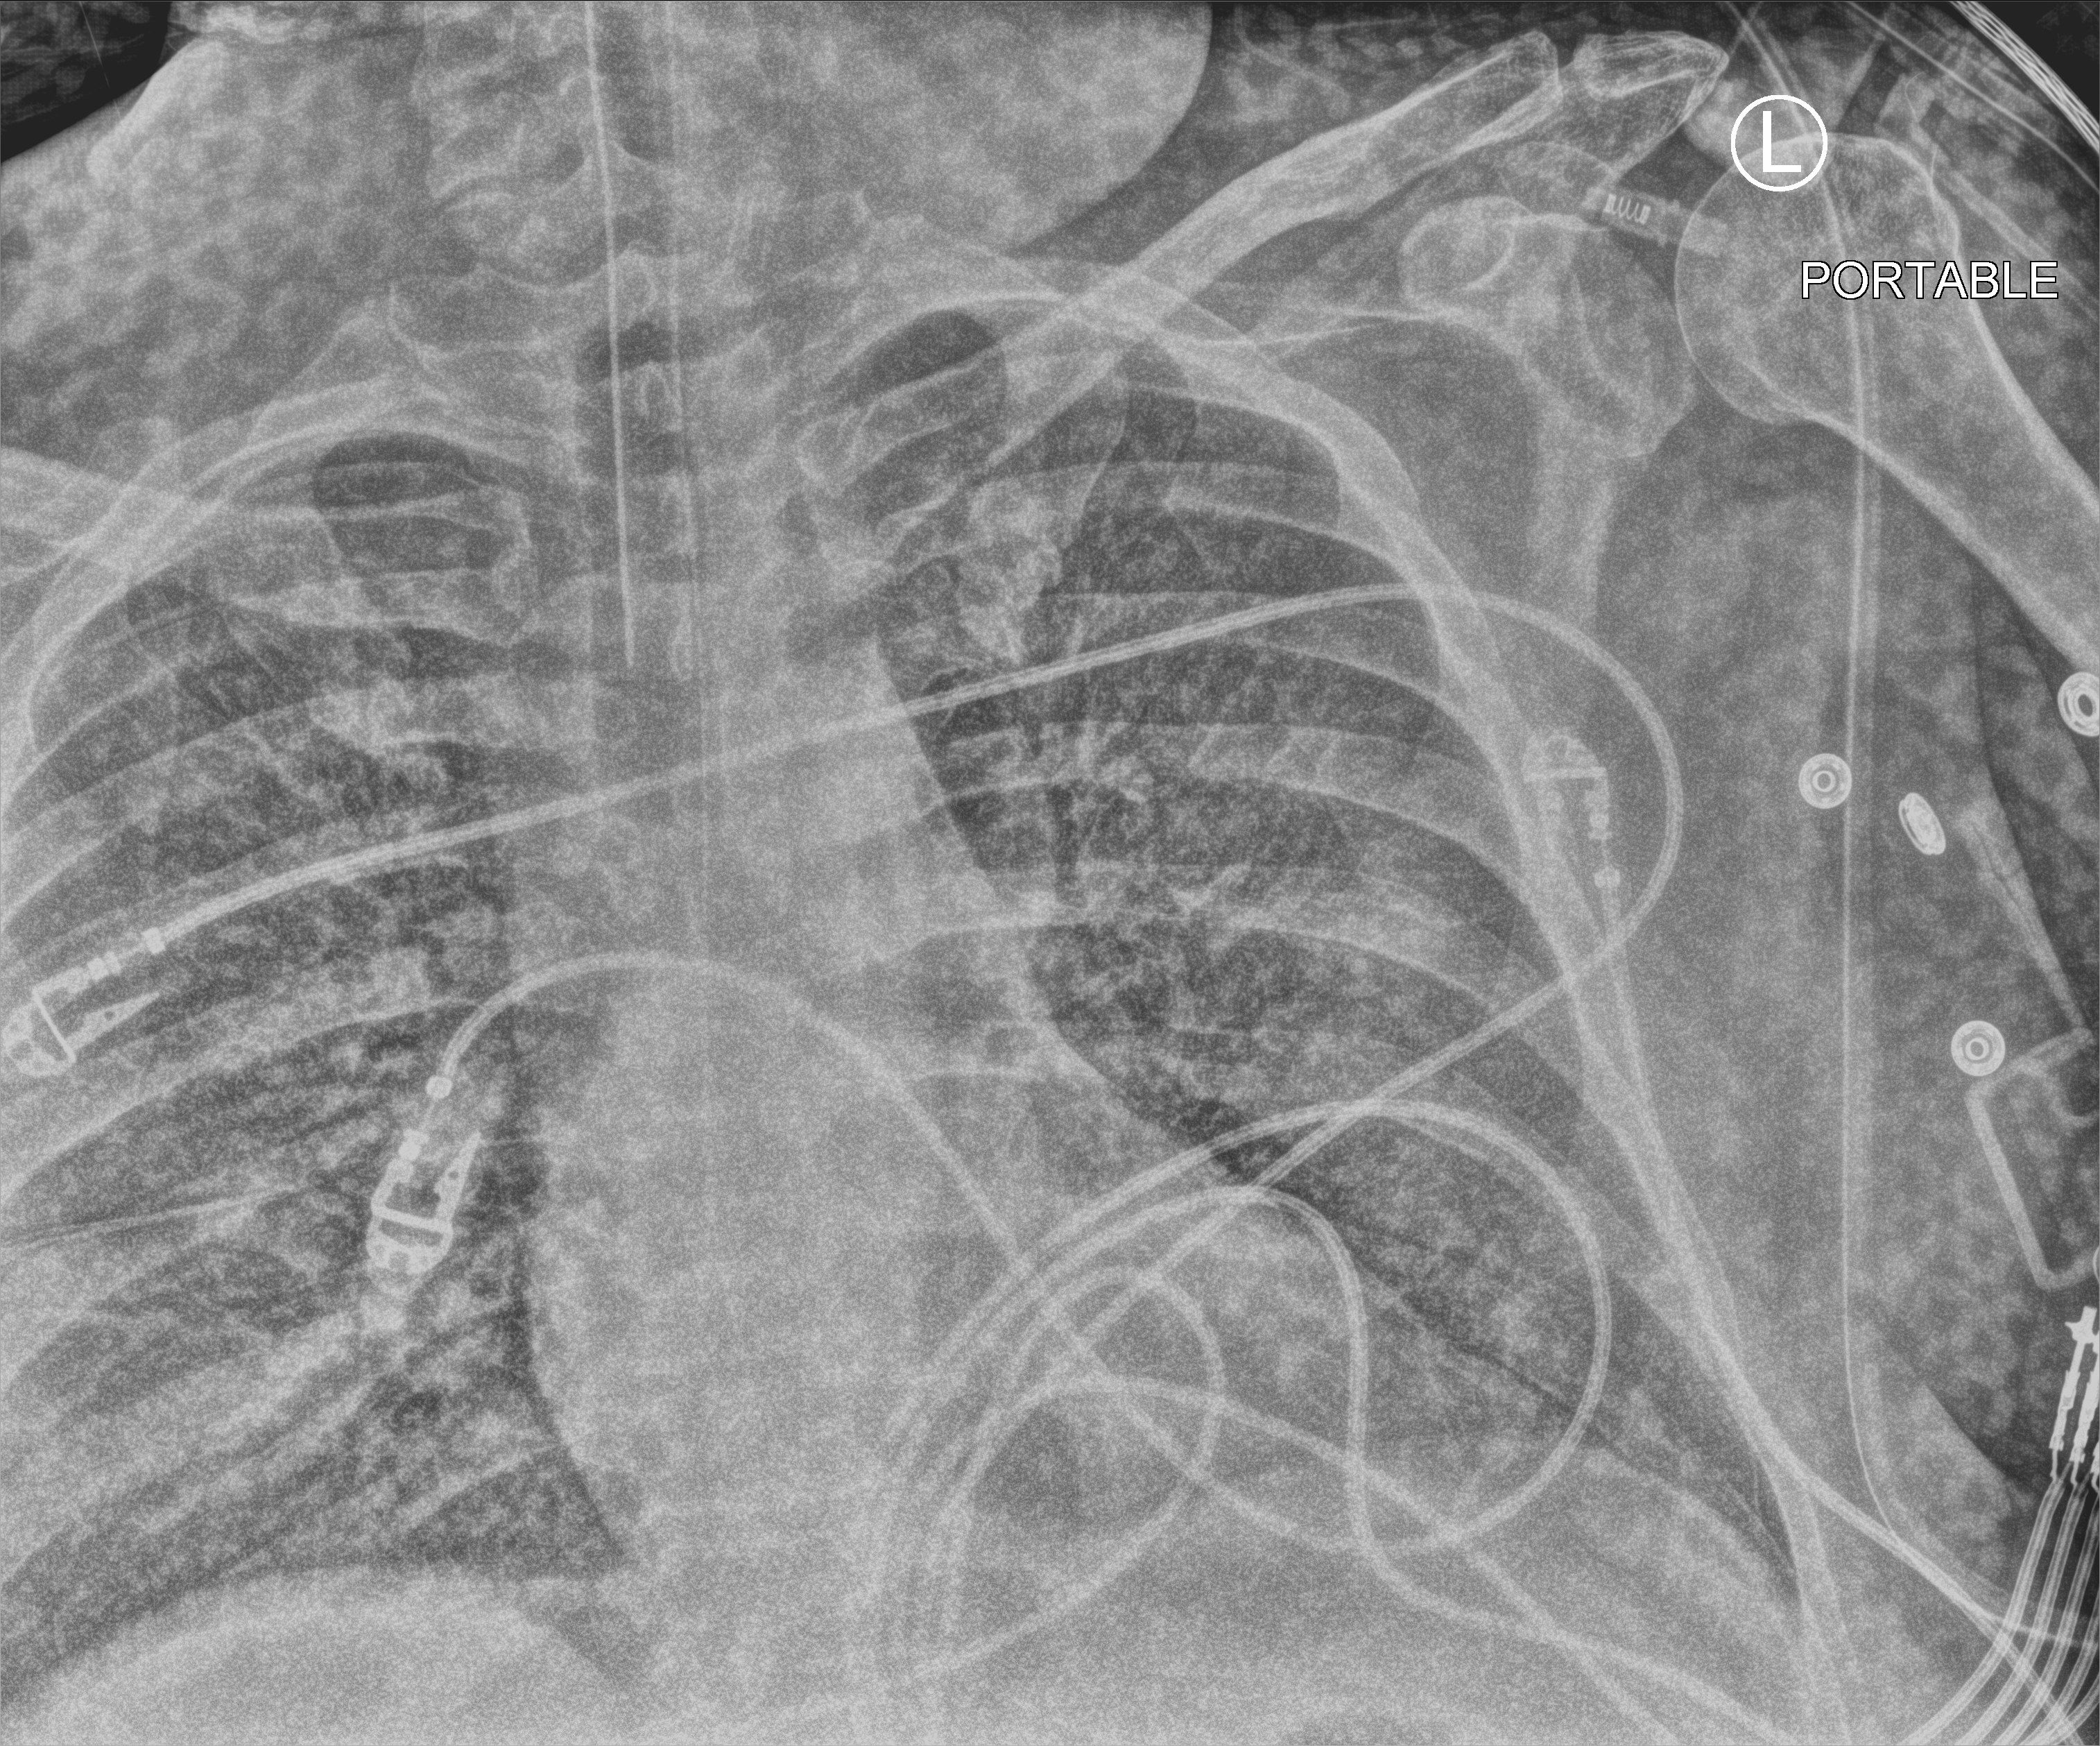
Portable chest radiograph, anteroposterior (AP) projection. Adult patient hospitalised with COVID-19, age 18–59 years.
Admission-level facts for this patient (not findings on this image; timing relative to this image not recorded): admitted to intensive care during this hospital stay: yes; chronic kidney disease (admission record): no; hypertension (admission record): yes.